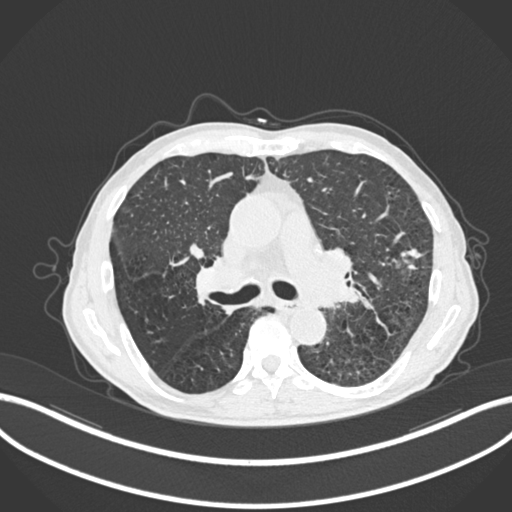
Chest CT, one axial slice. Slice 153 of 287 in the series (ordered by position). Reconstruction kernel B30f. 120 kVp. Lung window (W 1500 / L -600 HU). 1 mm slice thickness. 512 × 512 image matrix, field of view 400 × 400 mm. Male patient, age 74 years. From the clinical record (not read from this slice): clinical TNM (as recorded): T2a N1 M0.
Structures marked on this image (bounding box drawn by a radiologist):
- lung tumour (recorded histology: adenocarcinoma): bounding box (x1, y1, x2, y2) in pixels: (394, 239, 426, 276)